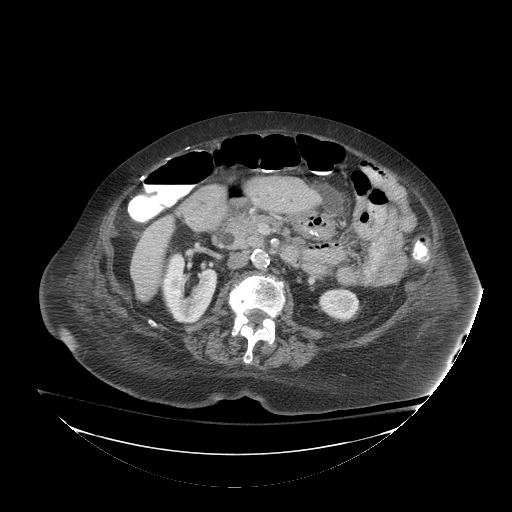
Contrast-enhanced abdominal CT (liver protocol), one axial slice. Position 26 of 81 along the scan axis. Soft-tissue window (W 400 / L 40 HU). 2.5 mm slice thickness. 512 × 512 image matrix, field of view 500 × 500 mm. Case-level facts recorded for this patient, not image findings: diagnosis: hepatocellular carcinoma (patient treated with transarterial chemoembolisation; whether this scan precedes or follows treatment is not stated here); TNM stage (as recorded): Stage-I; Child-Pugh class: B; tumour differentiation: well-moderately differentiated.
Annotated regions visible in this slice (semi-automatically segmented with operator editing):
- liver parenchyma outside the tumour (the mass and vessels are separate outlines, so this box may not span the whole liver): bounding box [x1, y1, x2, y2] px = [130, 216, 174, 276]